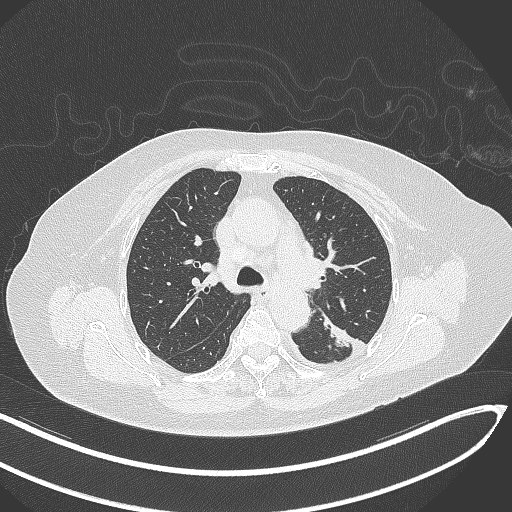
Chest CT, one axial slice; position 213 of 270 along the scan axis; reconstruction kernel B70f; 120 kVp; lung window (W 1500 / L -600 HU); 1 mm slice thickness; 512 × 512 image matrix. Female patient, age 76 years. Case-level facts recorded for this patient, not image findings: clinical TNM (as recorded): T1c N0 M0.
Outlined on this slice (rectangle marked by the reading radiologist):
- lung tumour (recorded histology: adenocarcinoma): bounding box <317,314,355,352> (left, top, right, bottom; pixels)